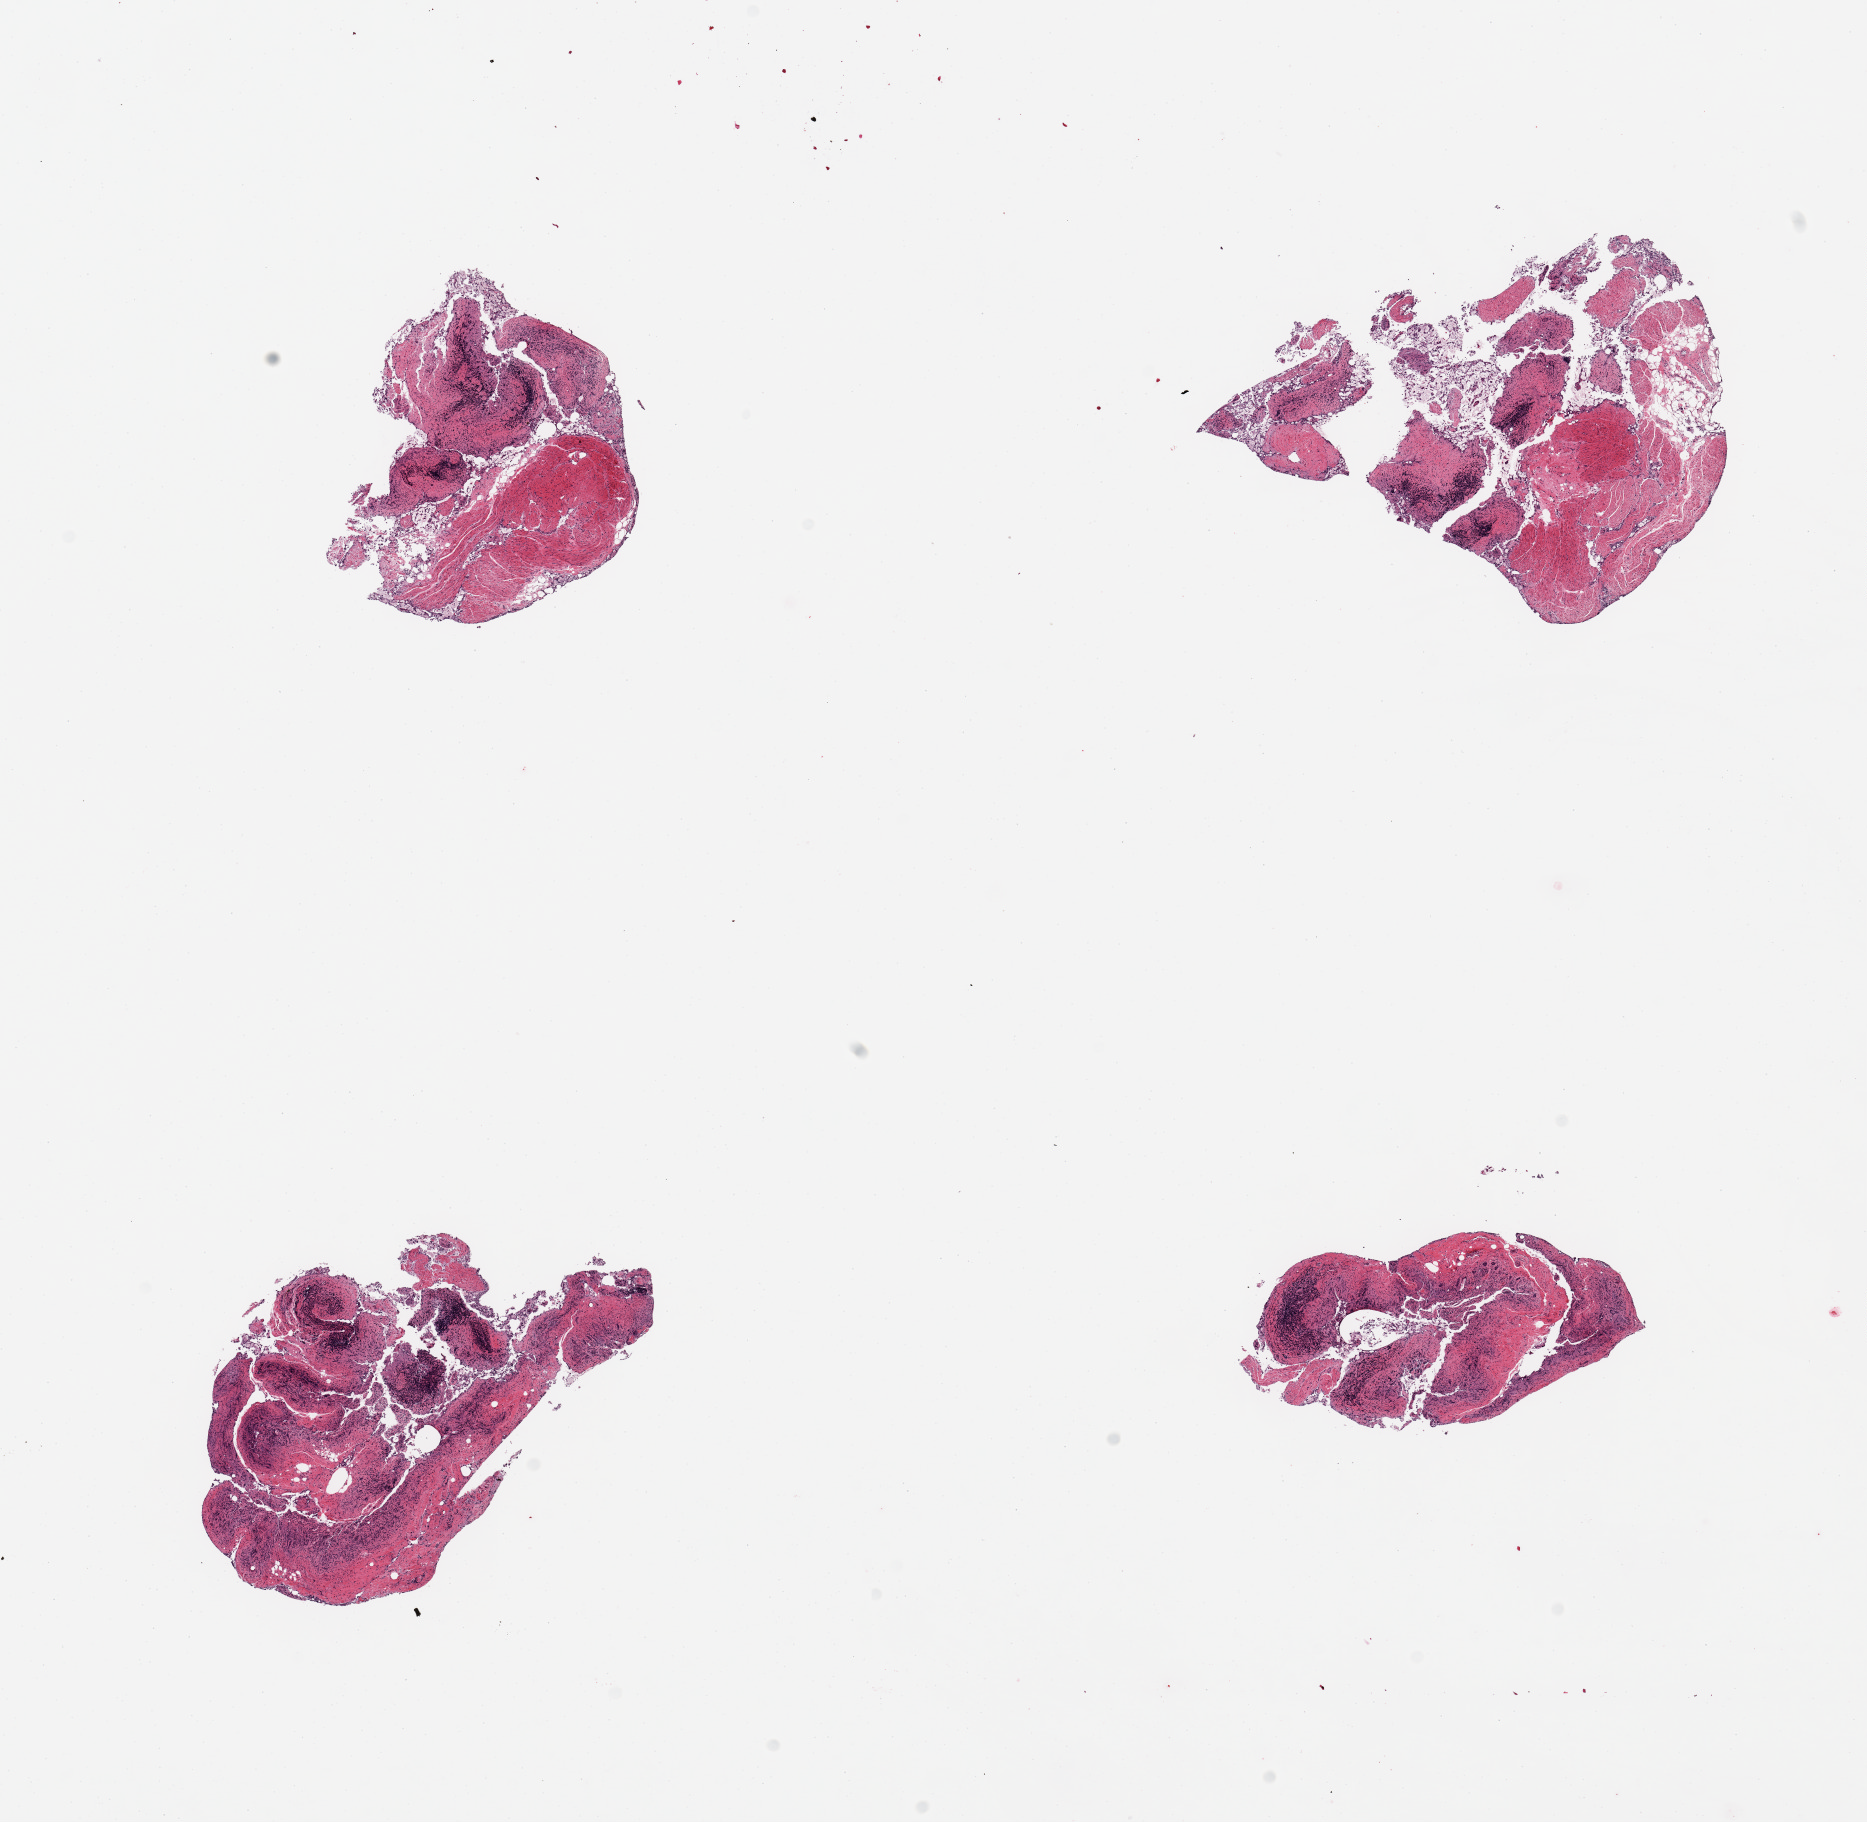
Whole-slide image, H&E stain — shown as a low-resolution overview of the whole scanned area (about 14.8 x 14.4 mm), PAXgene-fixed, paraffin-embedded tissue, target tissue: ileum, donor tissue sample. Donor sex: male.
Review note (as recorded): 4 pieces, totally autolyzed, correct target but too few lymphoid aggregates to warrant analysis (~5%).